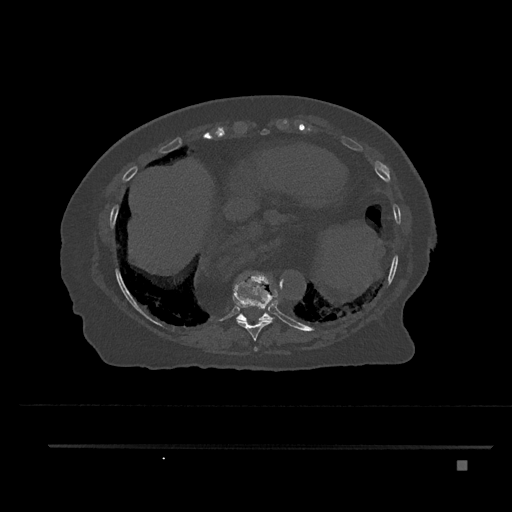
CT including the spine, one axial slice. Reconstruction kernel Br40s/3. 120 kVp. Bone window (W 1800 / L 400 HU). 0.5 mm slice thickness. 512 × 512 image matrix. Patient: female, 76 years. Case-level facts recorded for this patient, not image findings: primary cancer: lung.
Outlined on this slice (semi-automatically segmented with operator editing):
- T10 vertebra: bounding box (x1, y1, x2, y2) in pixels: (236, 293, 278, 323)
- T8 vertebra: (253, 347, 258, 351)
- T9 vertebra: (233, 272, 278, 341)